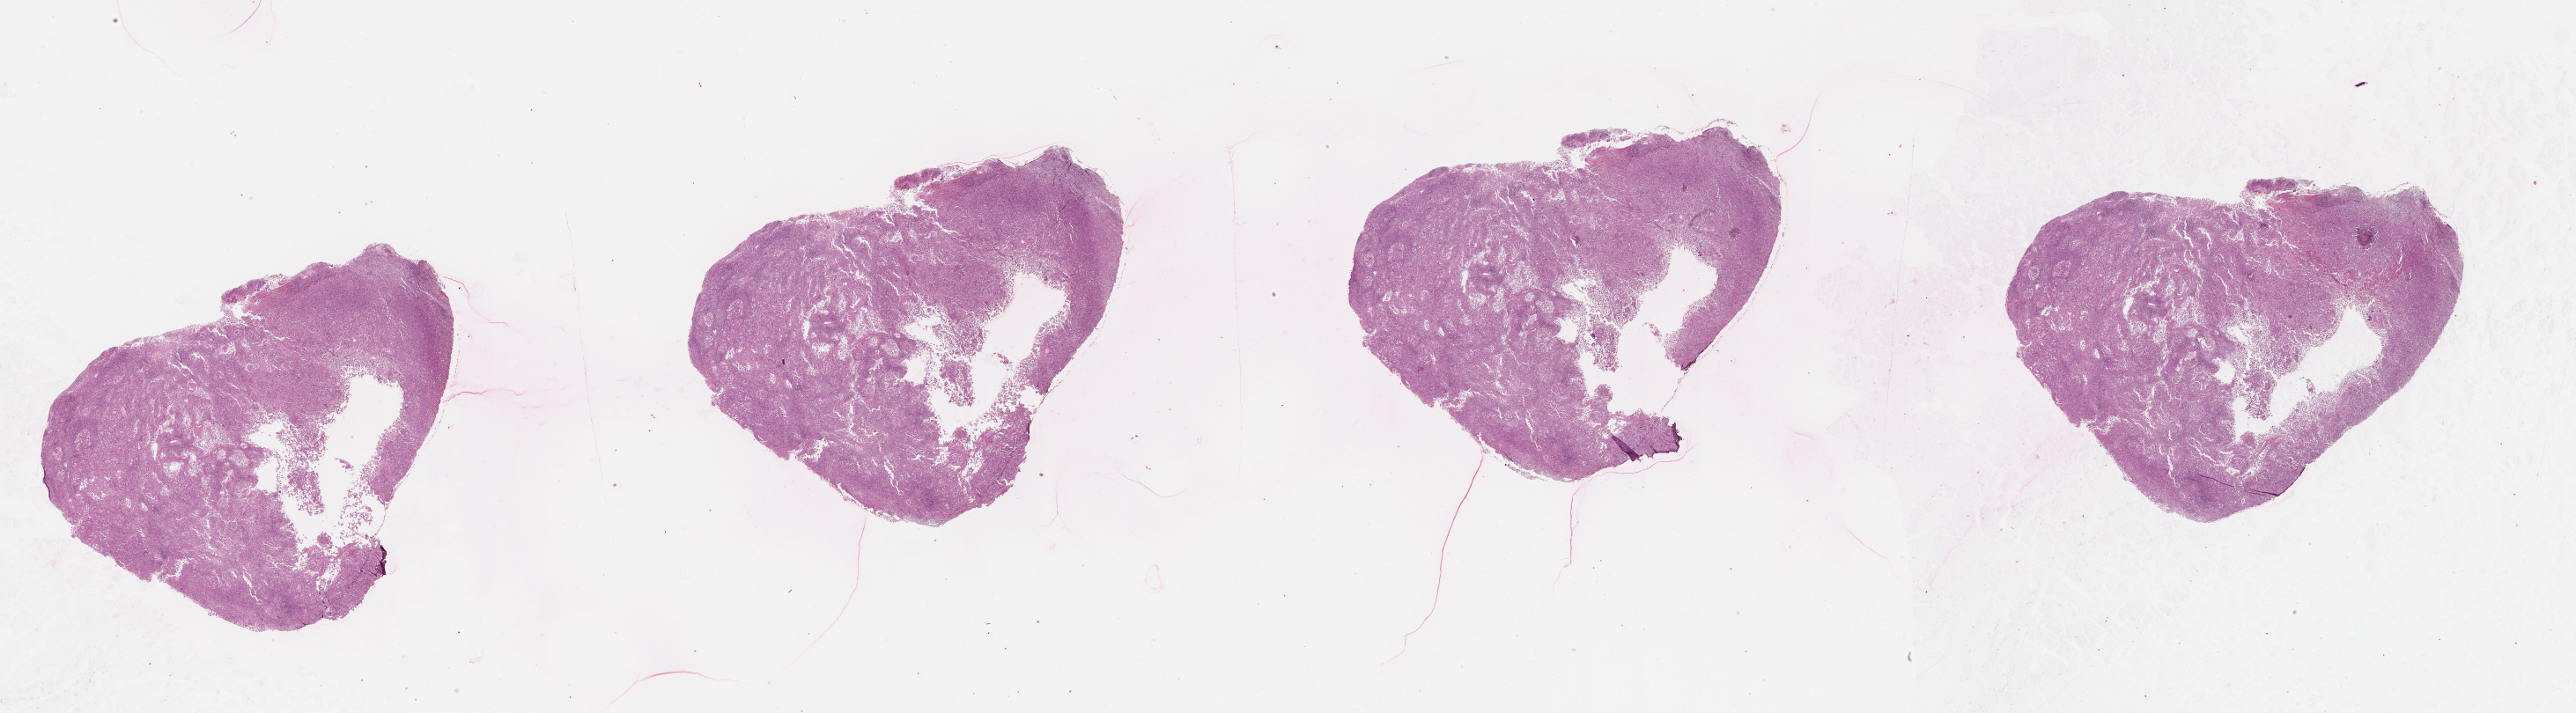
Whole-slide histology image, H&E — a low-resolution overview of the entire scanned area, about 47.1 x 13.0 mm (slide scanned at 20x). Male, 87 y/o.
Patient diagnosis: Malignant melanoma, NOS.